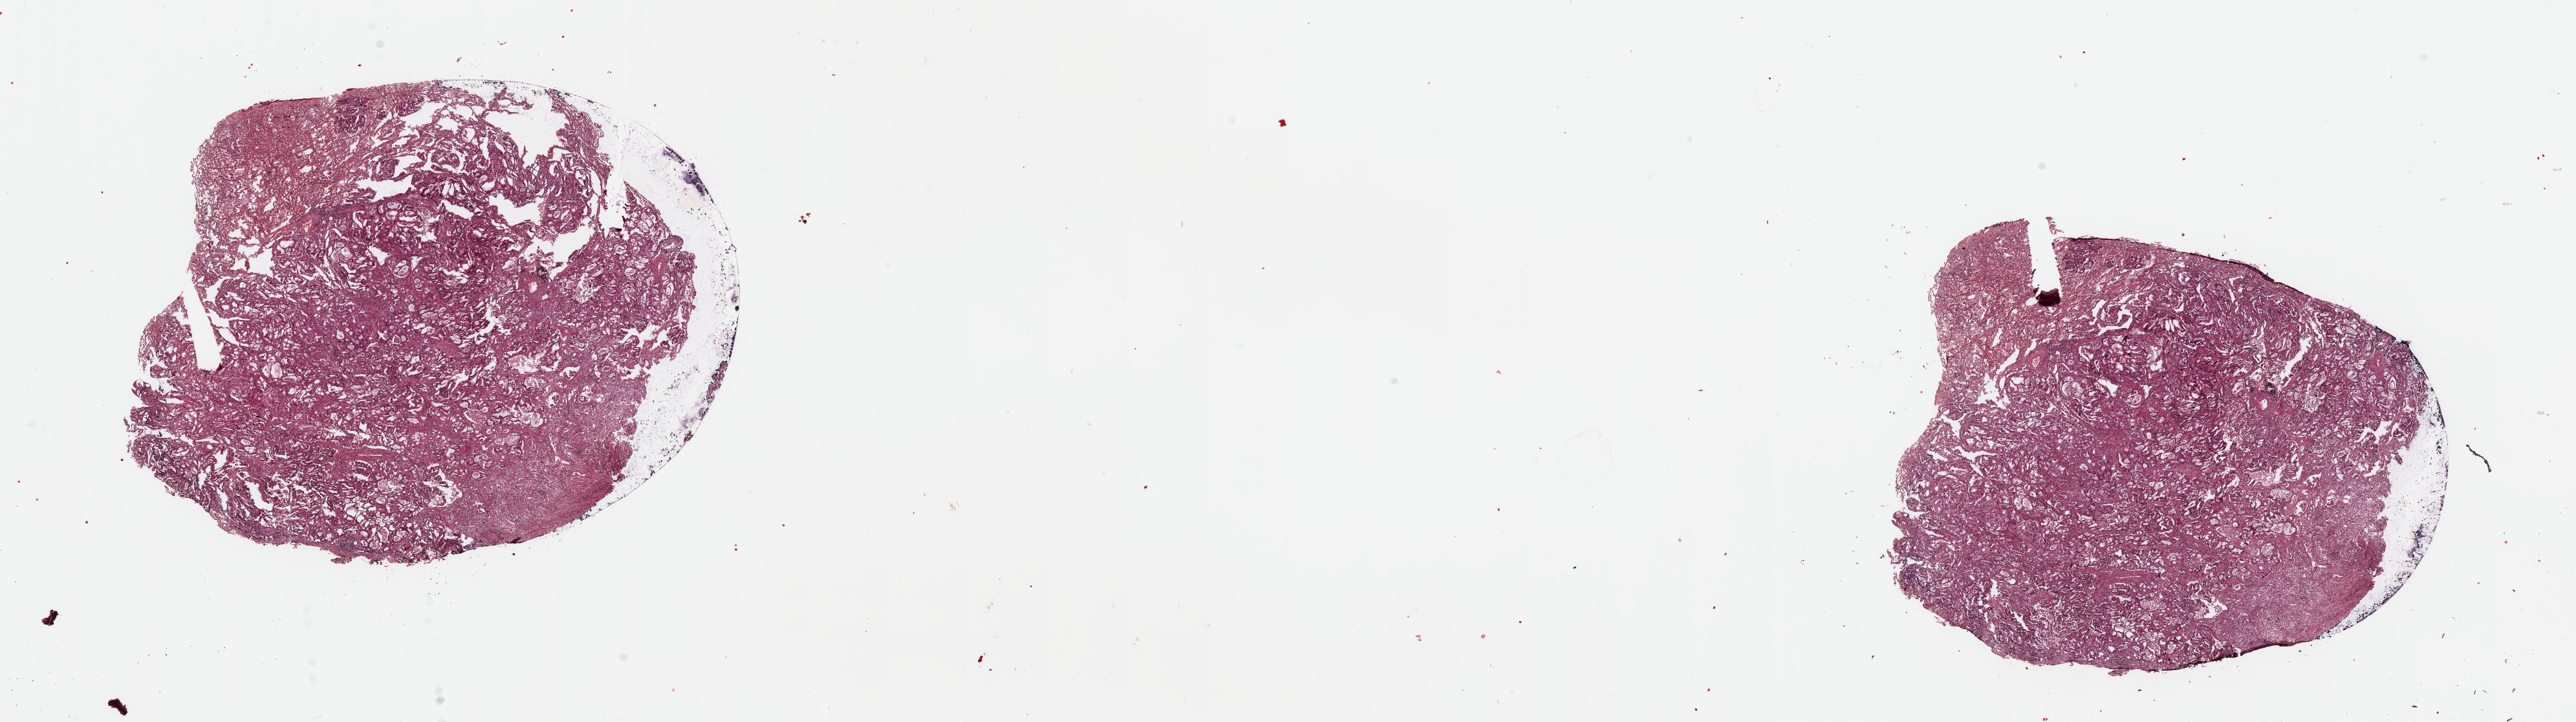
Whole-slide histology image, Hematoxylin and eosin (H&E) stained, a low-resolution overview of the entire scanned area, about 31.5 x 8.8 mm (acquisition: 20x scan), tumour tissue sample, sampled site: lung. 59-year-old male patient. Histologic grade: G2 (moderately differentiated). Composition of this section per pathologist review: tumour nuclei 75%, necrosis 10%.
AJCC pathologic stage: IIIA. Diagnosis: Adenocarcinoma, NOS.